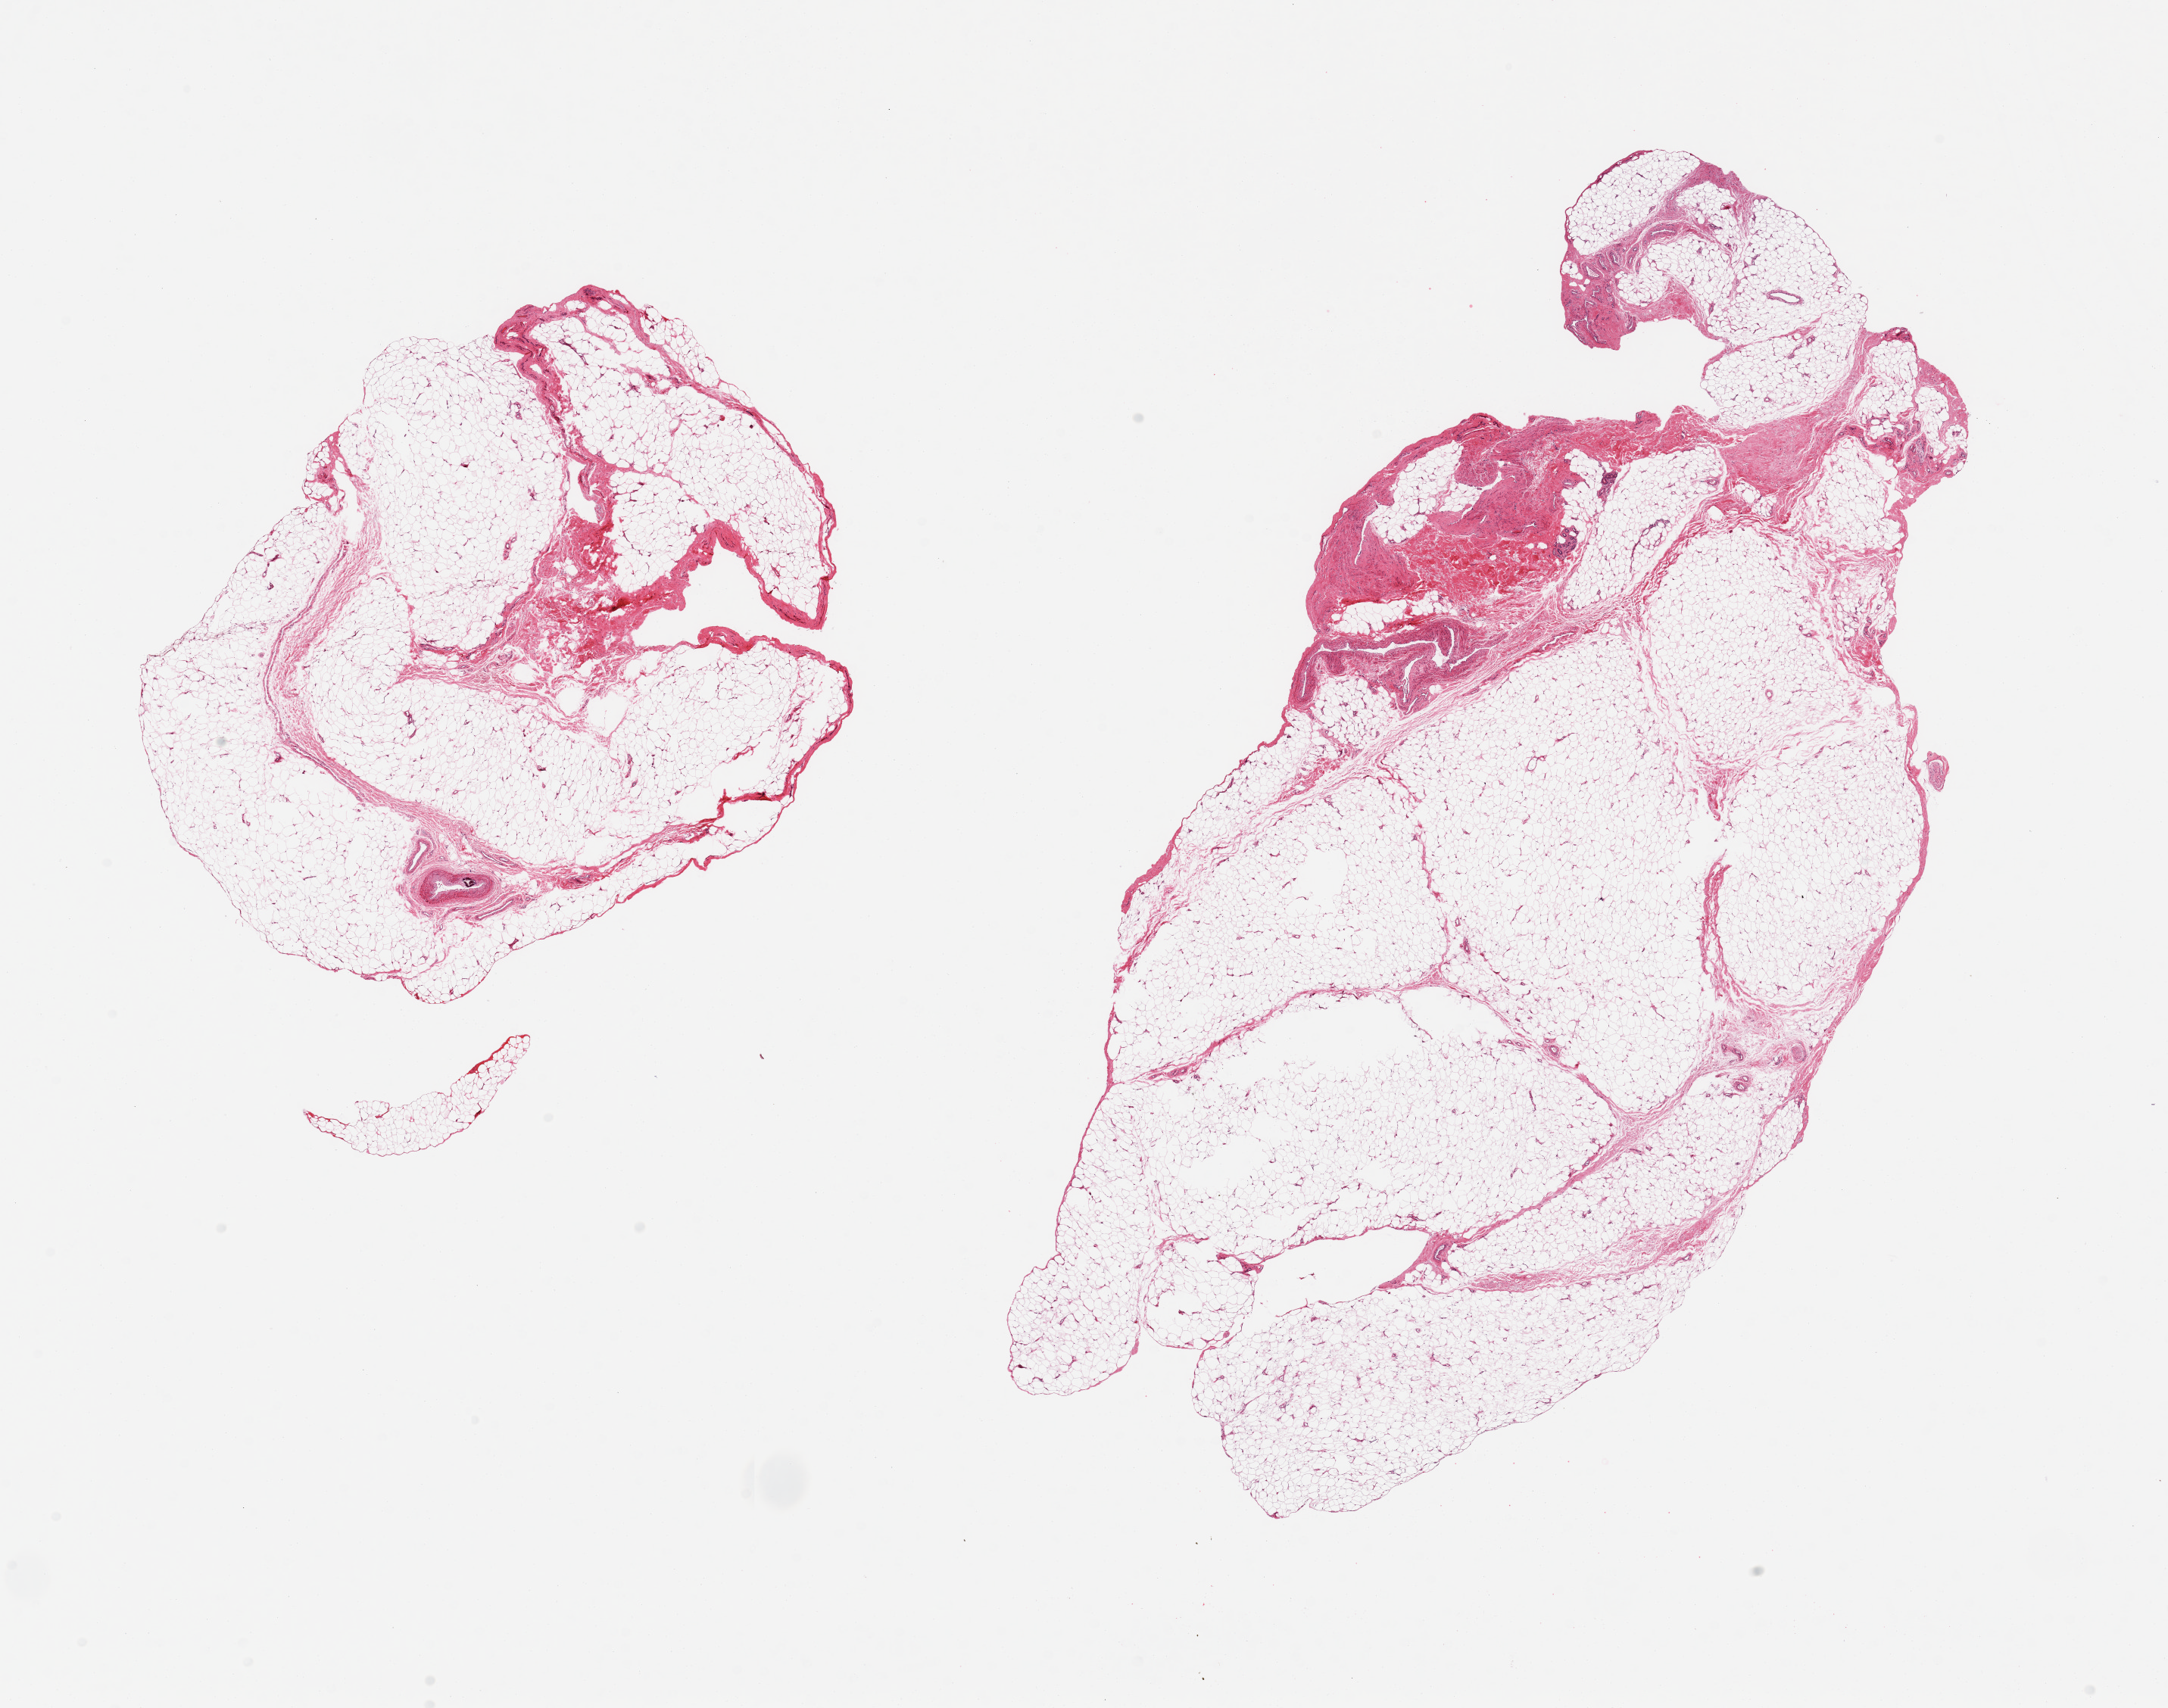
Digitized H&E-stained section — low-resolution overview of the scanned area, about 22.6 x 17.8 mm; PAXgene-fixed, paraffin-embedded tissue; sampled site (target tissue): adipose tissue; tissue donor sample. Male donor.
Reviewer comment on this tissue sample: 2 pieces; 10% fibrovascular content.